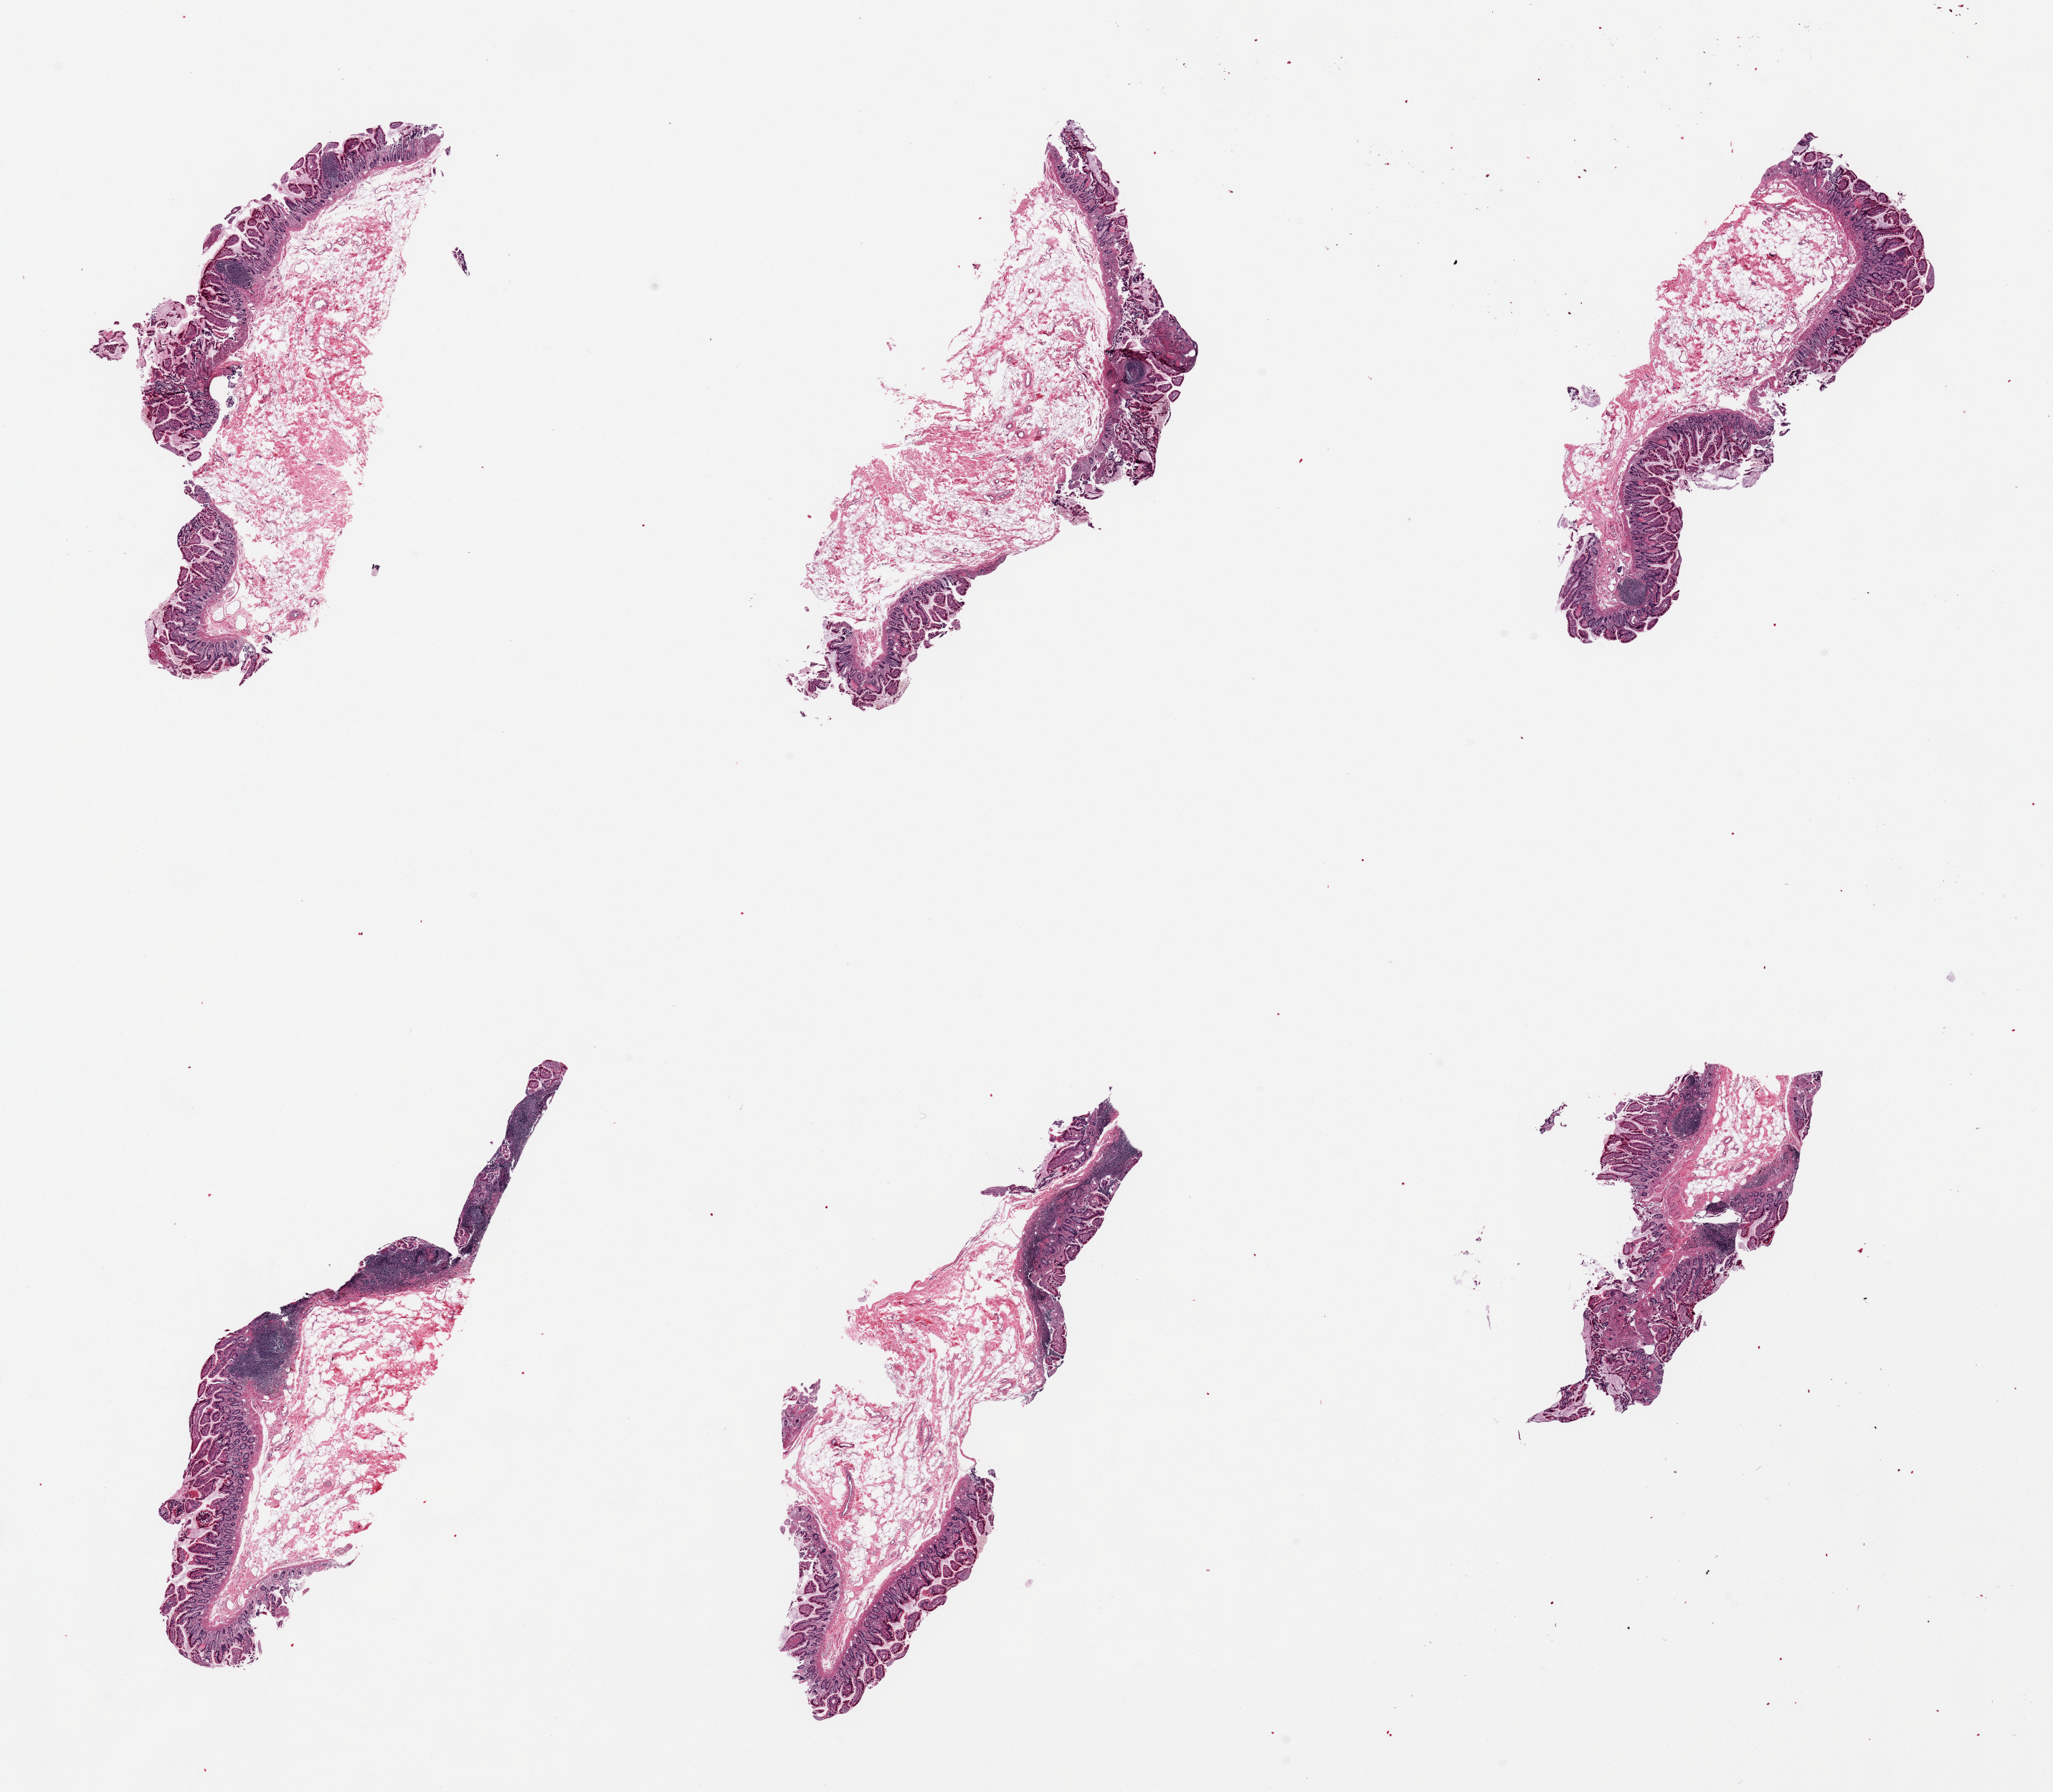
Whole-slide image, hematoxylin and eosin (H&E) stain, a low-resolution overview of the entire scanned area, about 22.6 x 19.8 mm, PAXgene-fixed, paraffin-embedded tissue, target tissue: ileum, tissue donor sample. Donor sex: male.
Review note (as recorded): 6 pieces; mucosa and submucosa, but with inconsistent lymphoid component, insufficient to warrant analysis.